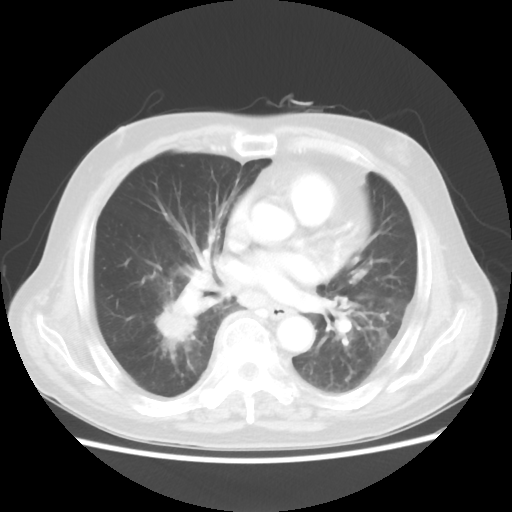
Chest CT, one axial slice. Reconstruction kernel STANDARD. 100 kVp. Lung window (W 1500 / L -600 HU). 5 mm slice thickness. 512 × 512 image matrix, field of view 359 × 359 mm. Male patient, age 83 years. Case-level facts recorded for this patient, not image findings: clinical TNM (as recorded): T2 N3 M0.
Structures marked on this image (bounding box drawn by a radiologist):
- lung tumour (recorded histology: adenocarcinoma): box from (x=145, y=285) to (x=200, y=351) px